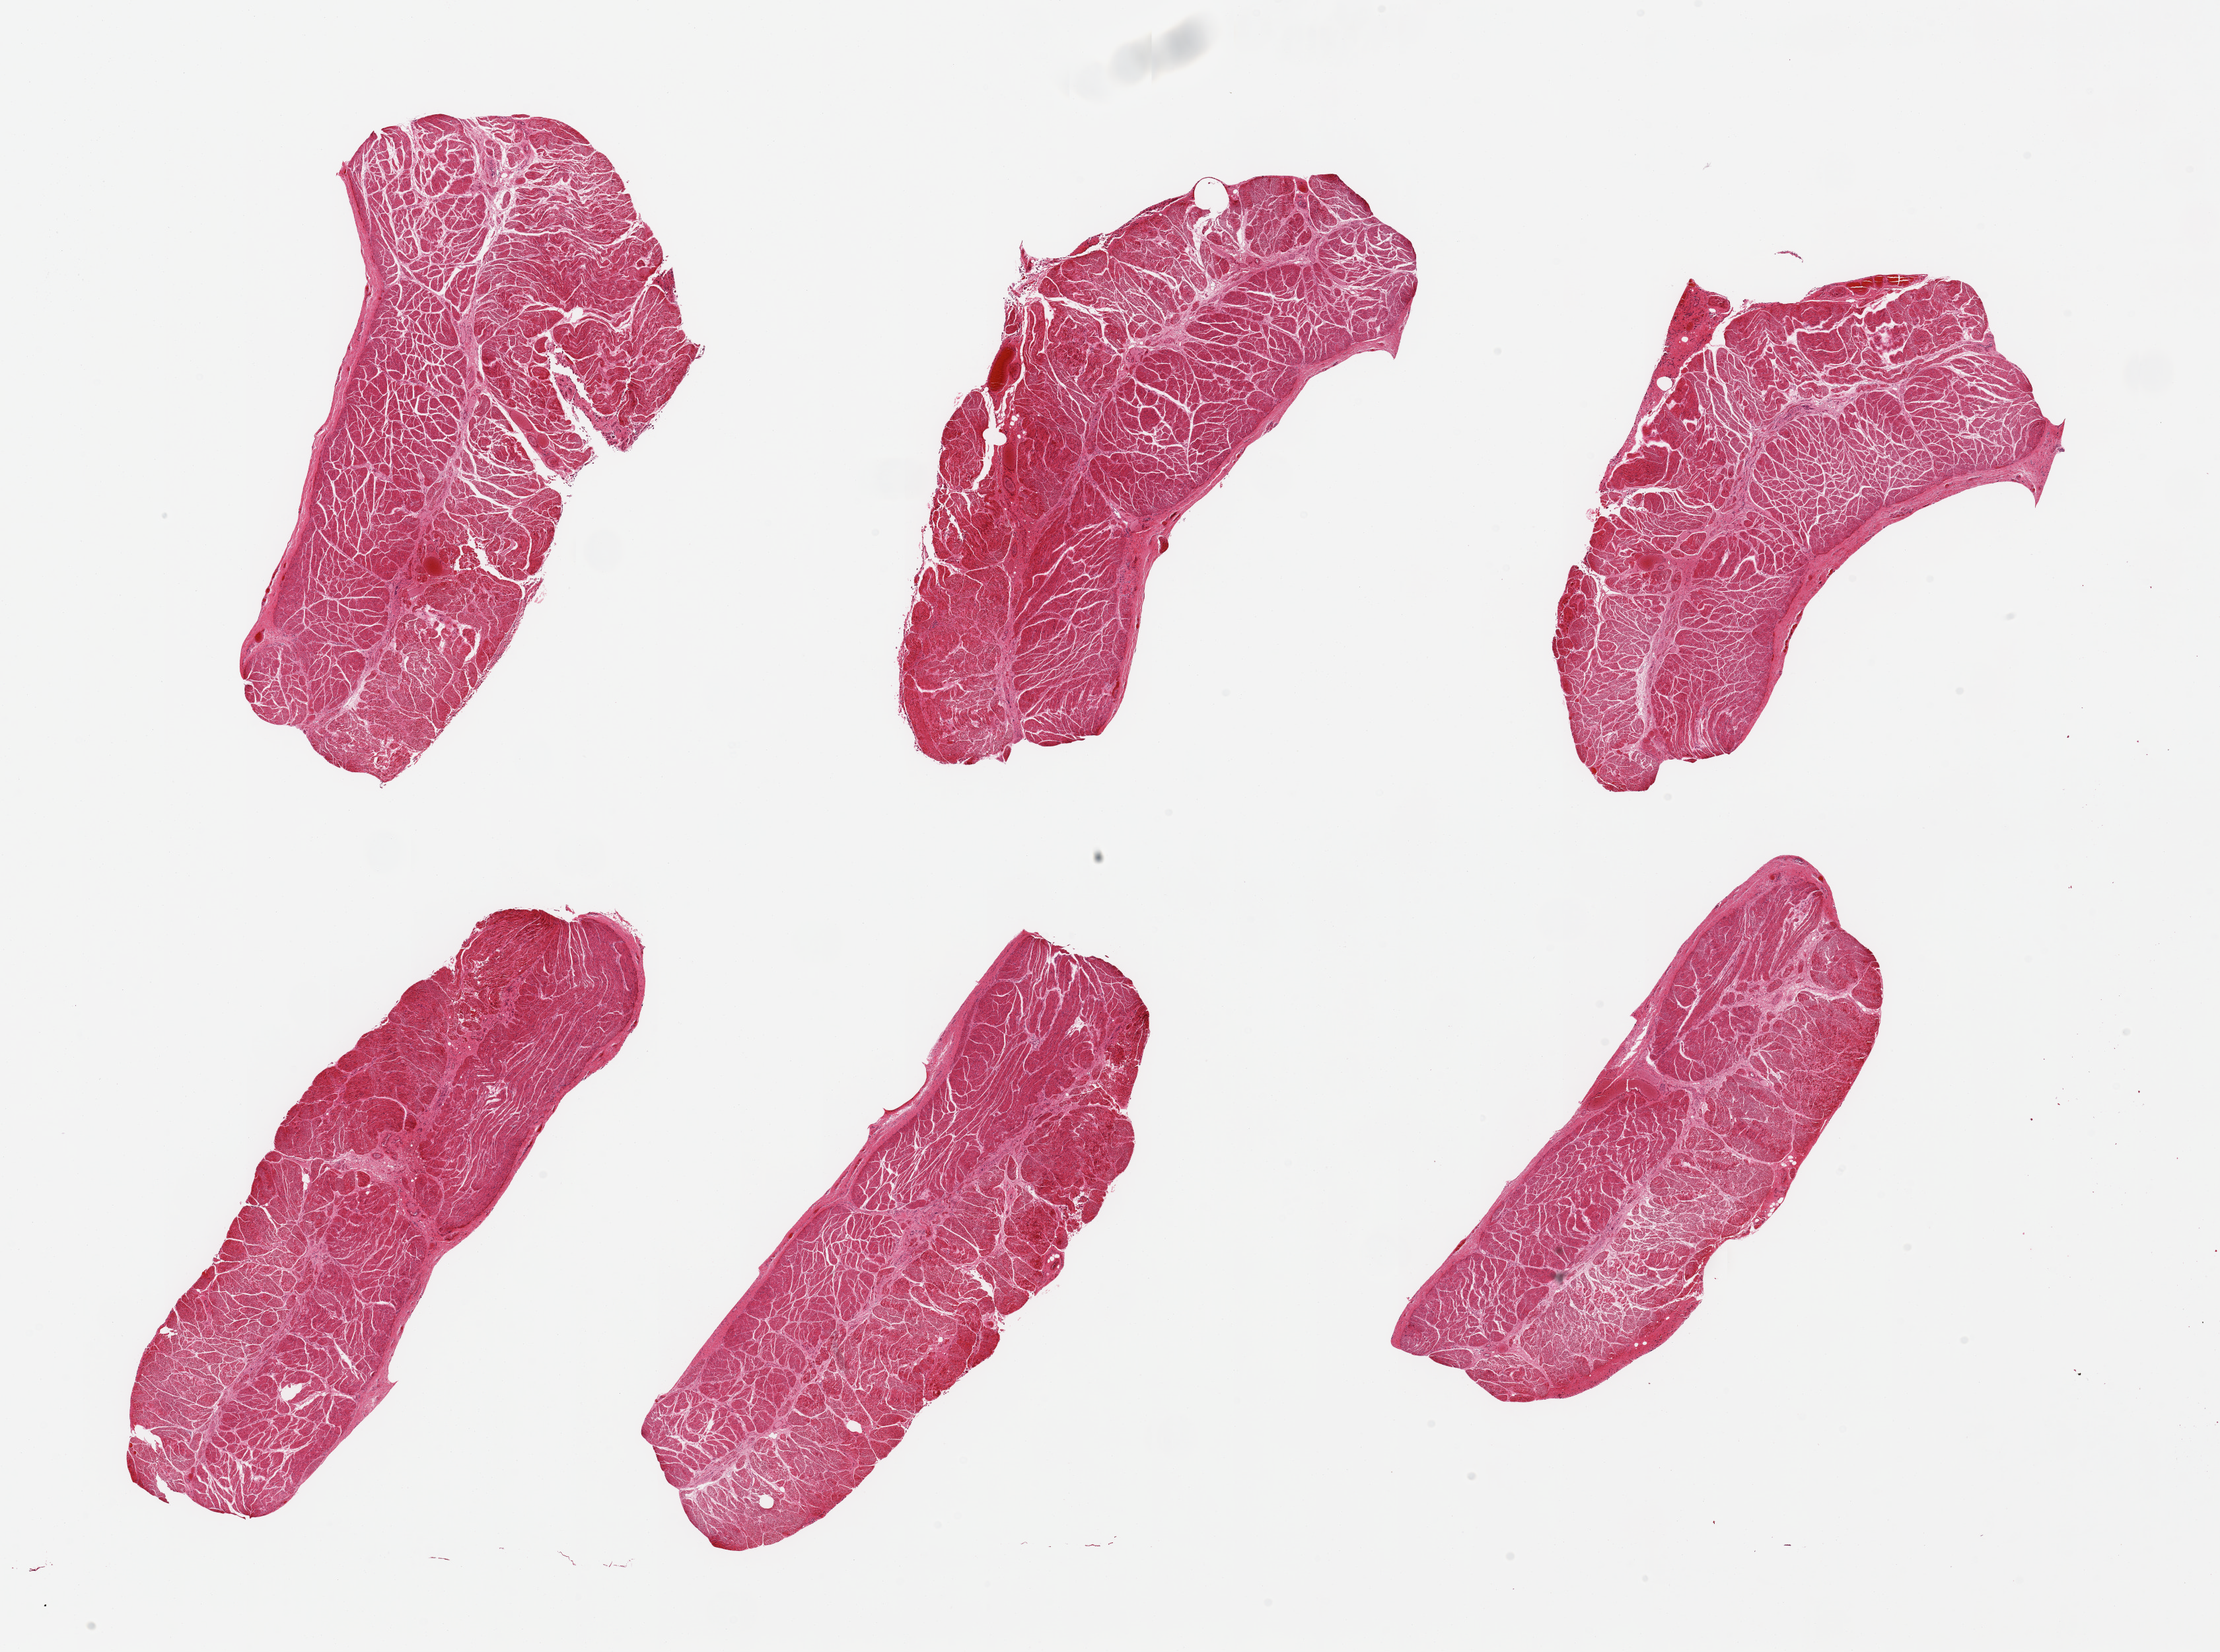
Digitized haematoxylin and eosin-stained section, whole scanned area (about 26.6 x 19.8 mm) shown as a low-resolution overview, PAXgene-fixed paraffin-embedded (PFPE) section, sampled site (target tissue): gastroesophageal junction, tissue donor sample.
- reviewer comment on this tissue sample: 6 pieces; well dissected muscularis